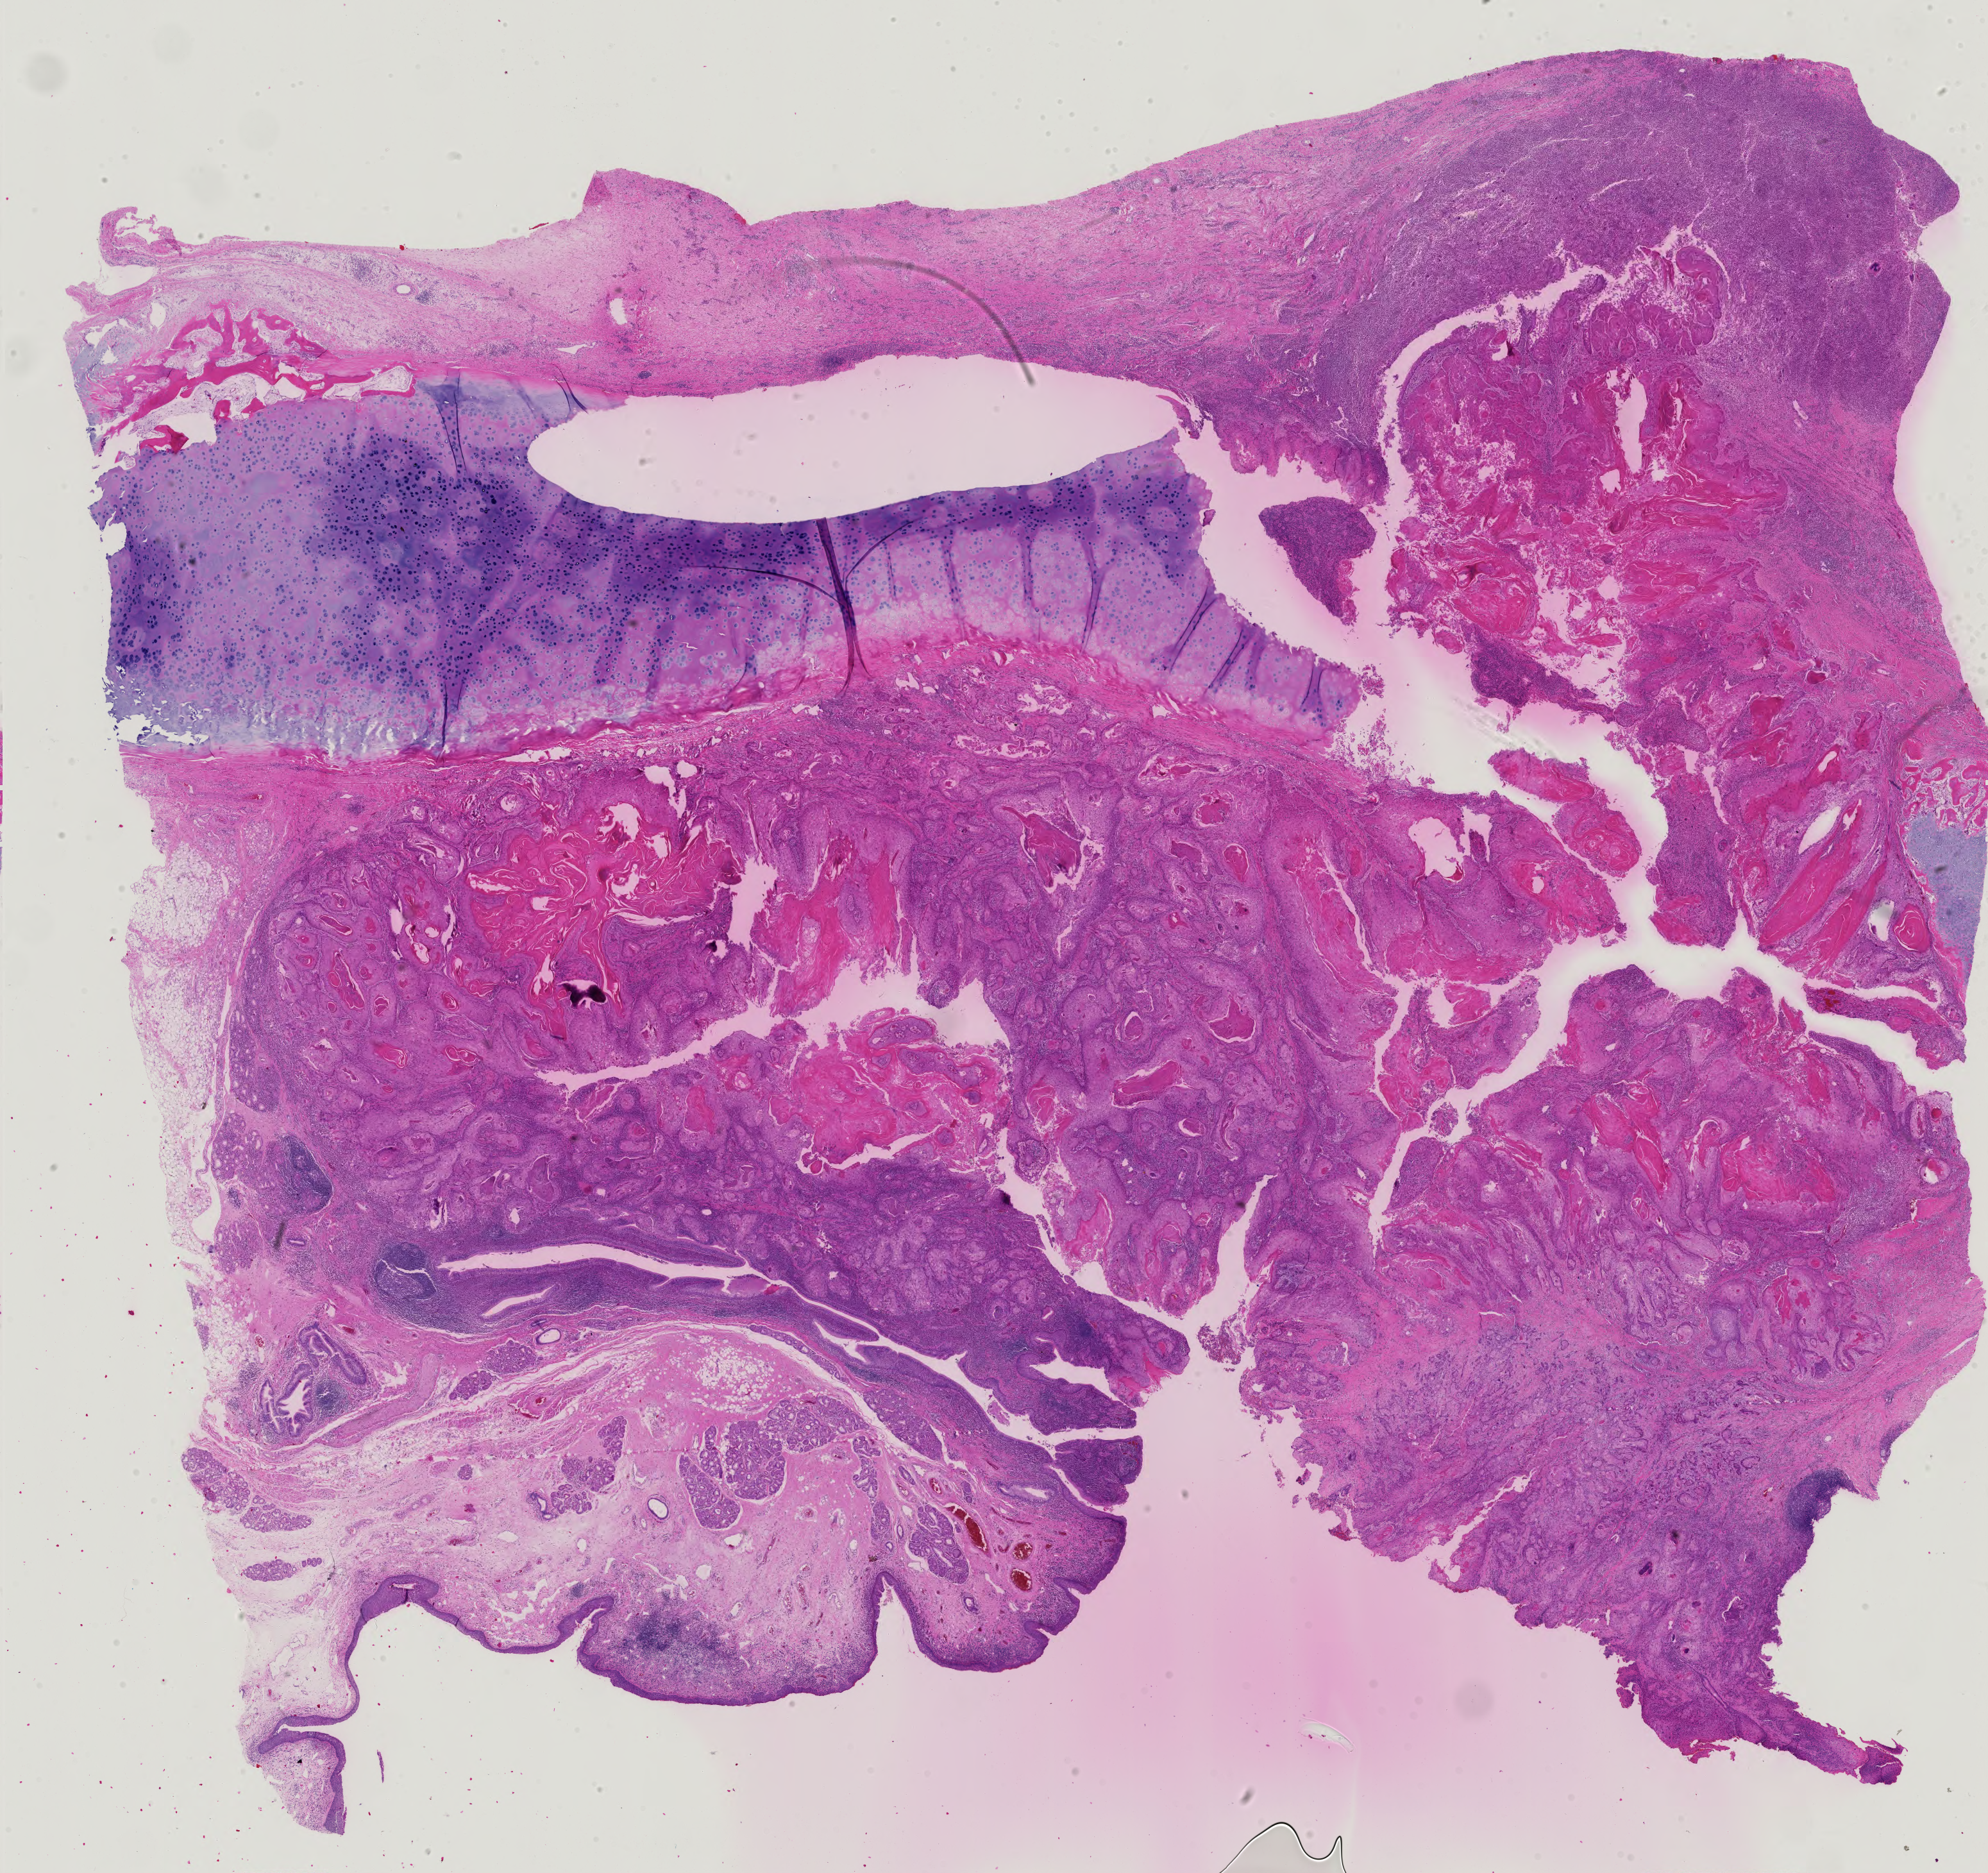
Digitized Hematoxylin and eosin (H&E) stained tissue section (whole slide), low-resolution overview of the scanned area, about 22.5 x 21.2 mm (slide scanned at 40x); formalin-fixed paraffin-embedded (FFPE) diagnostic section; sample: primary tumour, head and neck. Male patient; age at initial diagnosis 68 years. Histologic grade: G2 (moderately differentiated).
AJCC pathologic stage: IVA. Pathologic diagnosis: Squamous cell carcinoma, NOS.